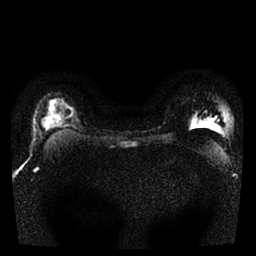
Breast MRI, one axial slice; diffusion-weighted series; image 2 of 4 stored at this slice position (different b-values; order by instance number); 1.5 T; 4 mm slice thickness; 256 × 256 image matrix, field of view 300 × 300 mm. Female patient.
Annotated regions visible in this slice (outlined manually by an expert reader):
- tumour on diffusion-weighted imaging: bounding box [x1, y1, x2, y2] px = [44, 121, 51, 127]